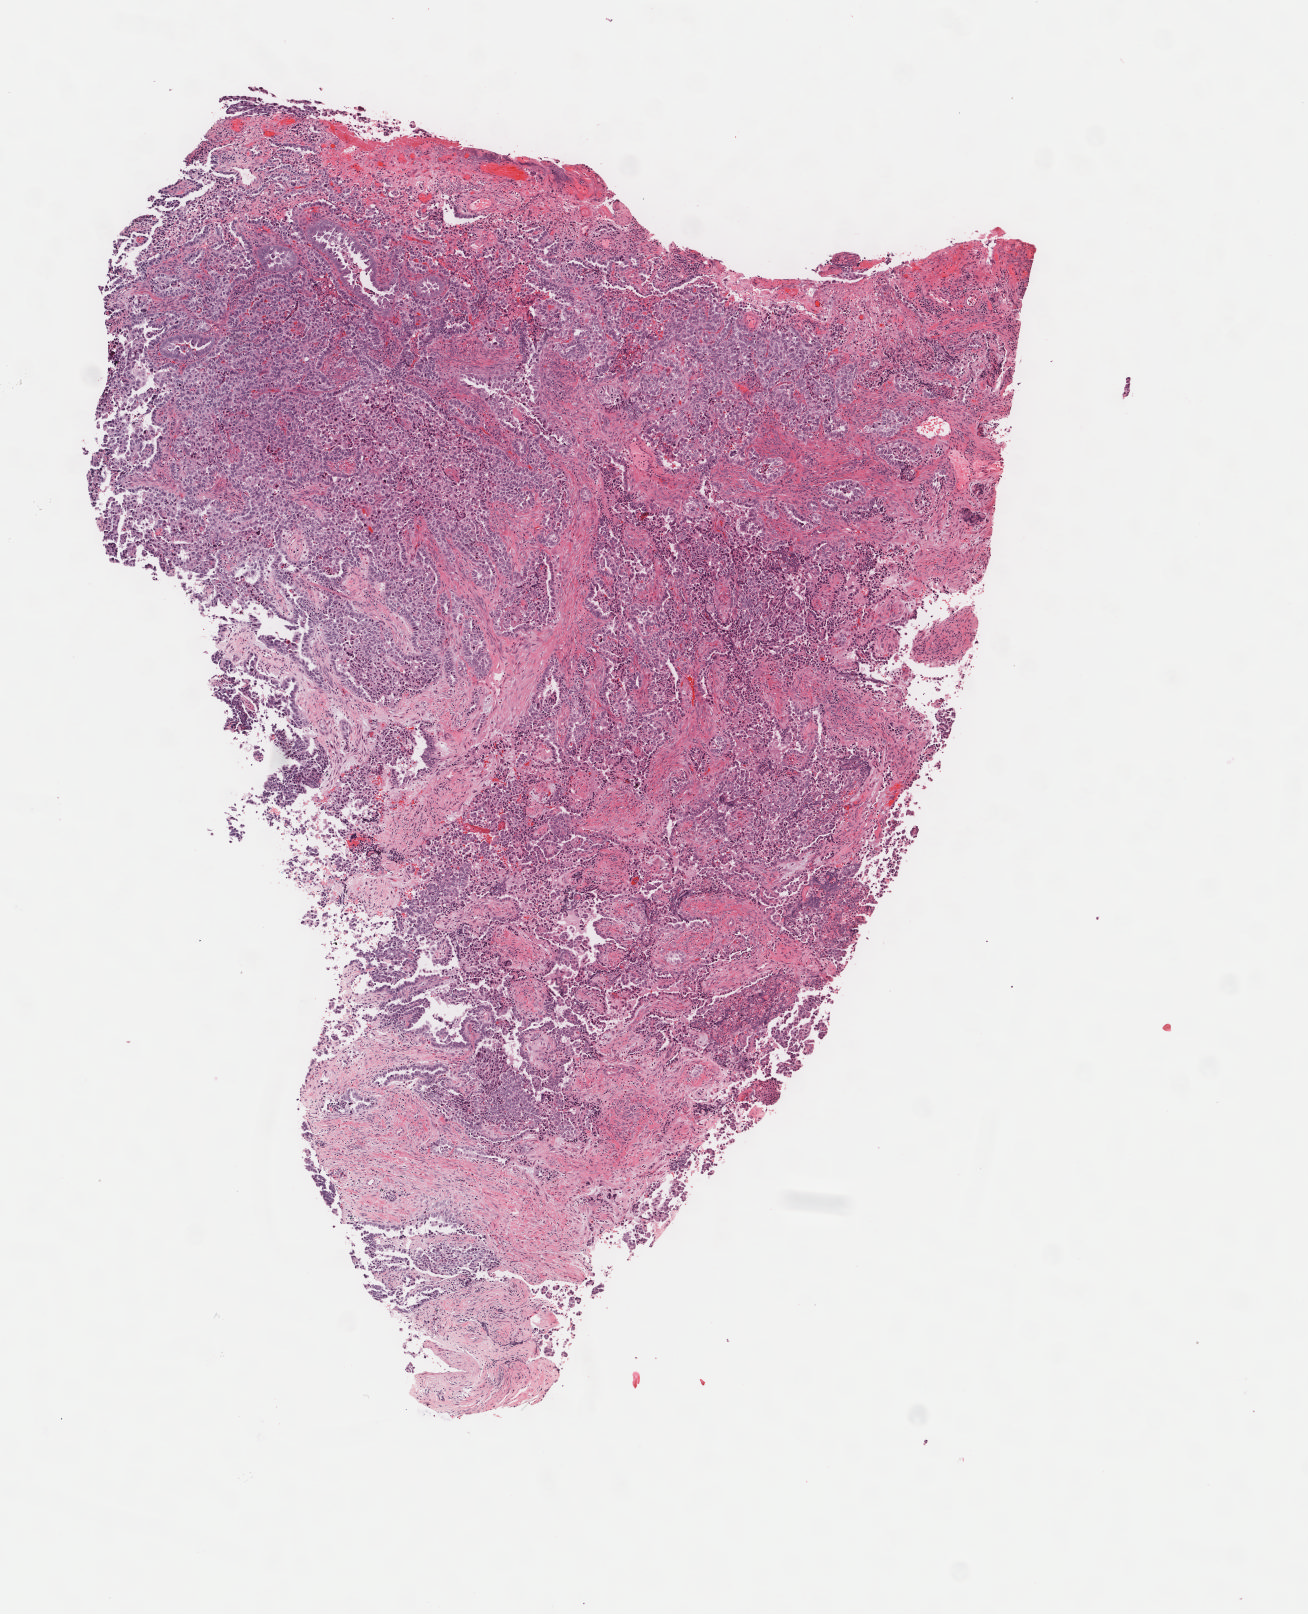
Digitized H&E-stained tissue section (whole slide), a low-resolution overview of the entire scanned area, about 5.2 x 6.4 mm (from a 40x scan), frozen section, primary tumour sample from the uterus. Female, age 69 years at initial diagnosis. Histologic grade: G3 (poorly differentiated). Composition of this section per pathologist review: tumour cells 100%, tumour nuclei 60%, normal cells 0%, stromal cells 0%, necrosis 0%. Inflammatory infiltration, as recorded: lymphocyte infiltration 4%, monocyte infiltration 0%, neutrophil infiltration 2%.
Diagnosis: Serous cystadenocarcinoma, NOS (endometrium). FIGO stage: IIIC.